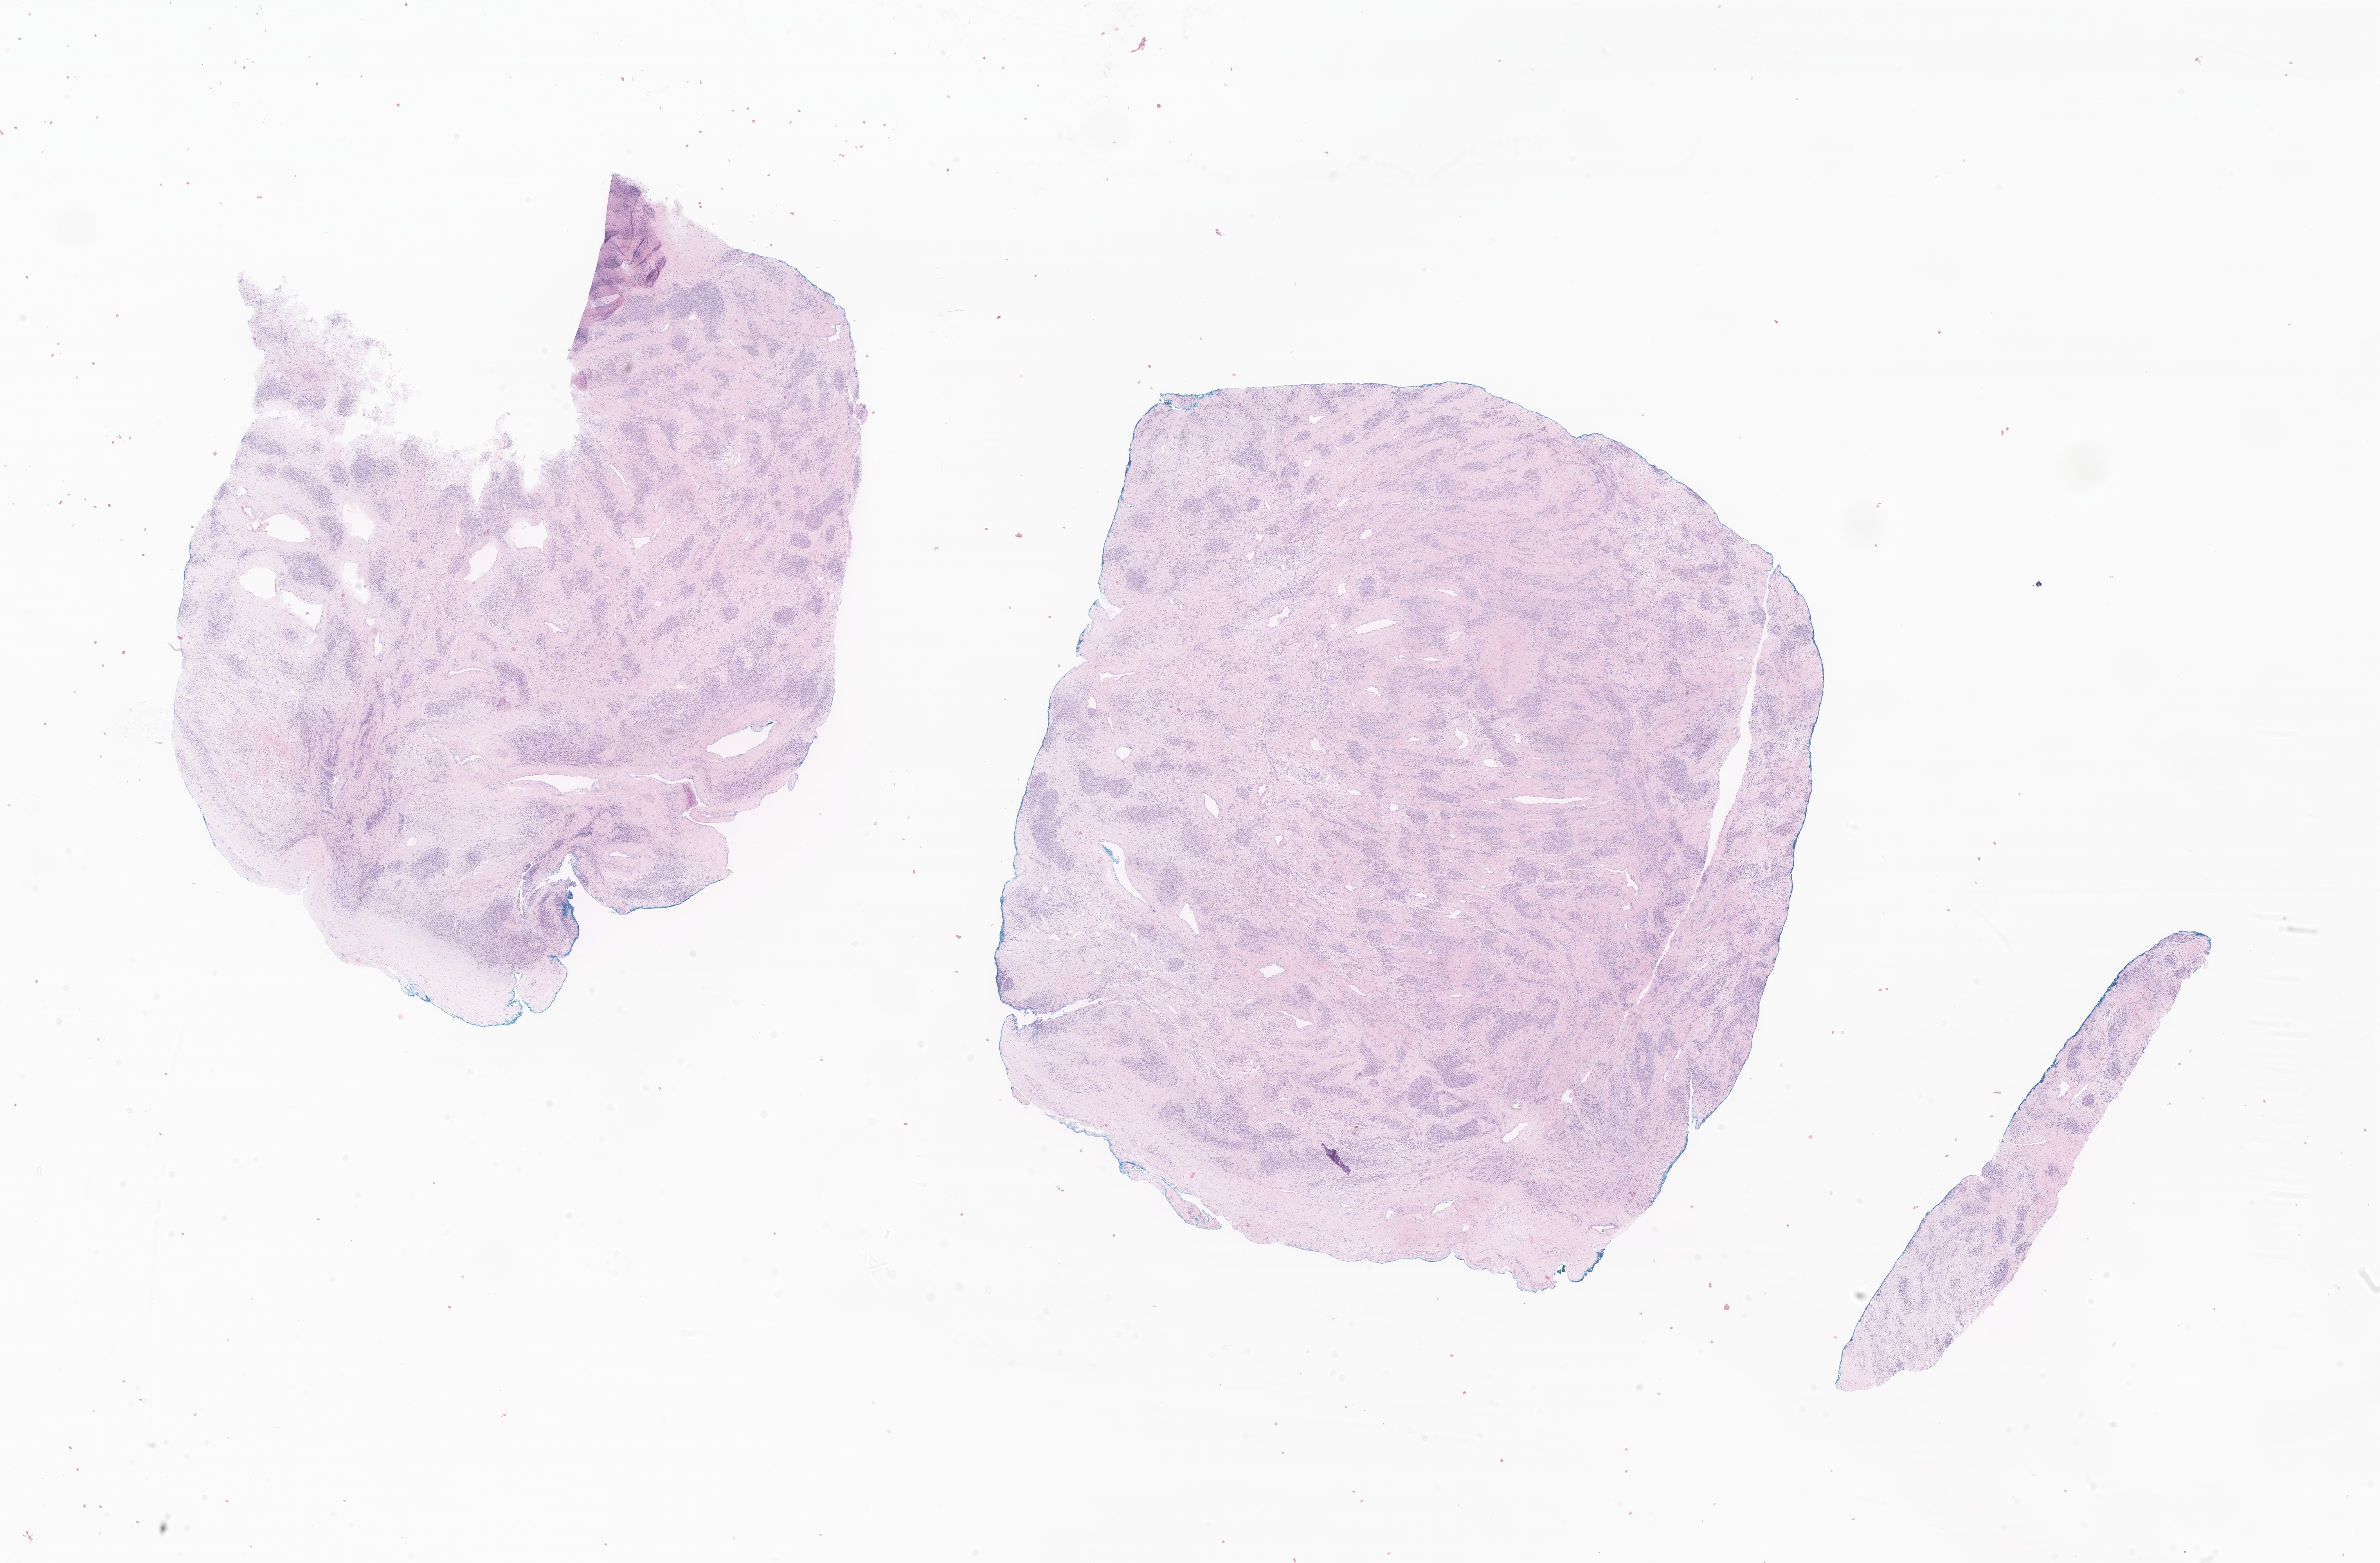
Digitized haematoxylin and eosin-stained section of tumor tissue from the abdomen, shown as a low-resolution overview of the whole scanned area (about 25.6 x 16.8 mm); formalin-fixed, paraffin-embedded (FFPE) tissue. Patient: male, age 995 days (about 2.7 years).
Diagnosis: Embryonal rhabdomyosarcoma, NOS.